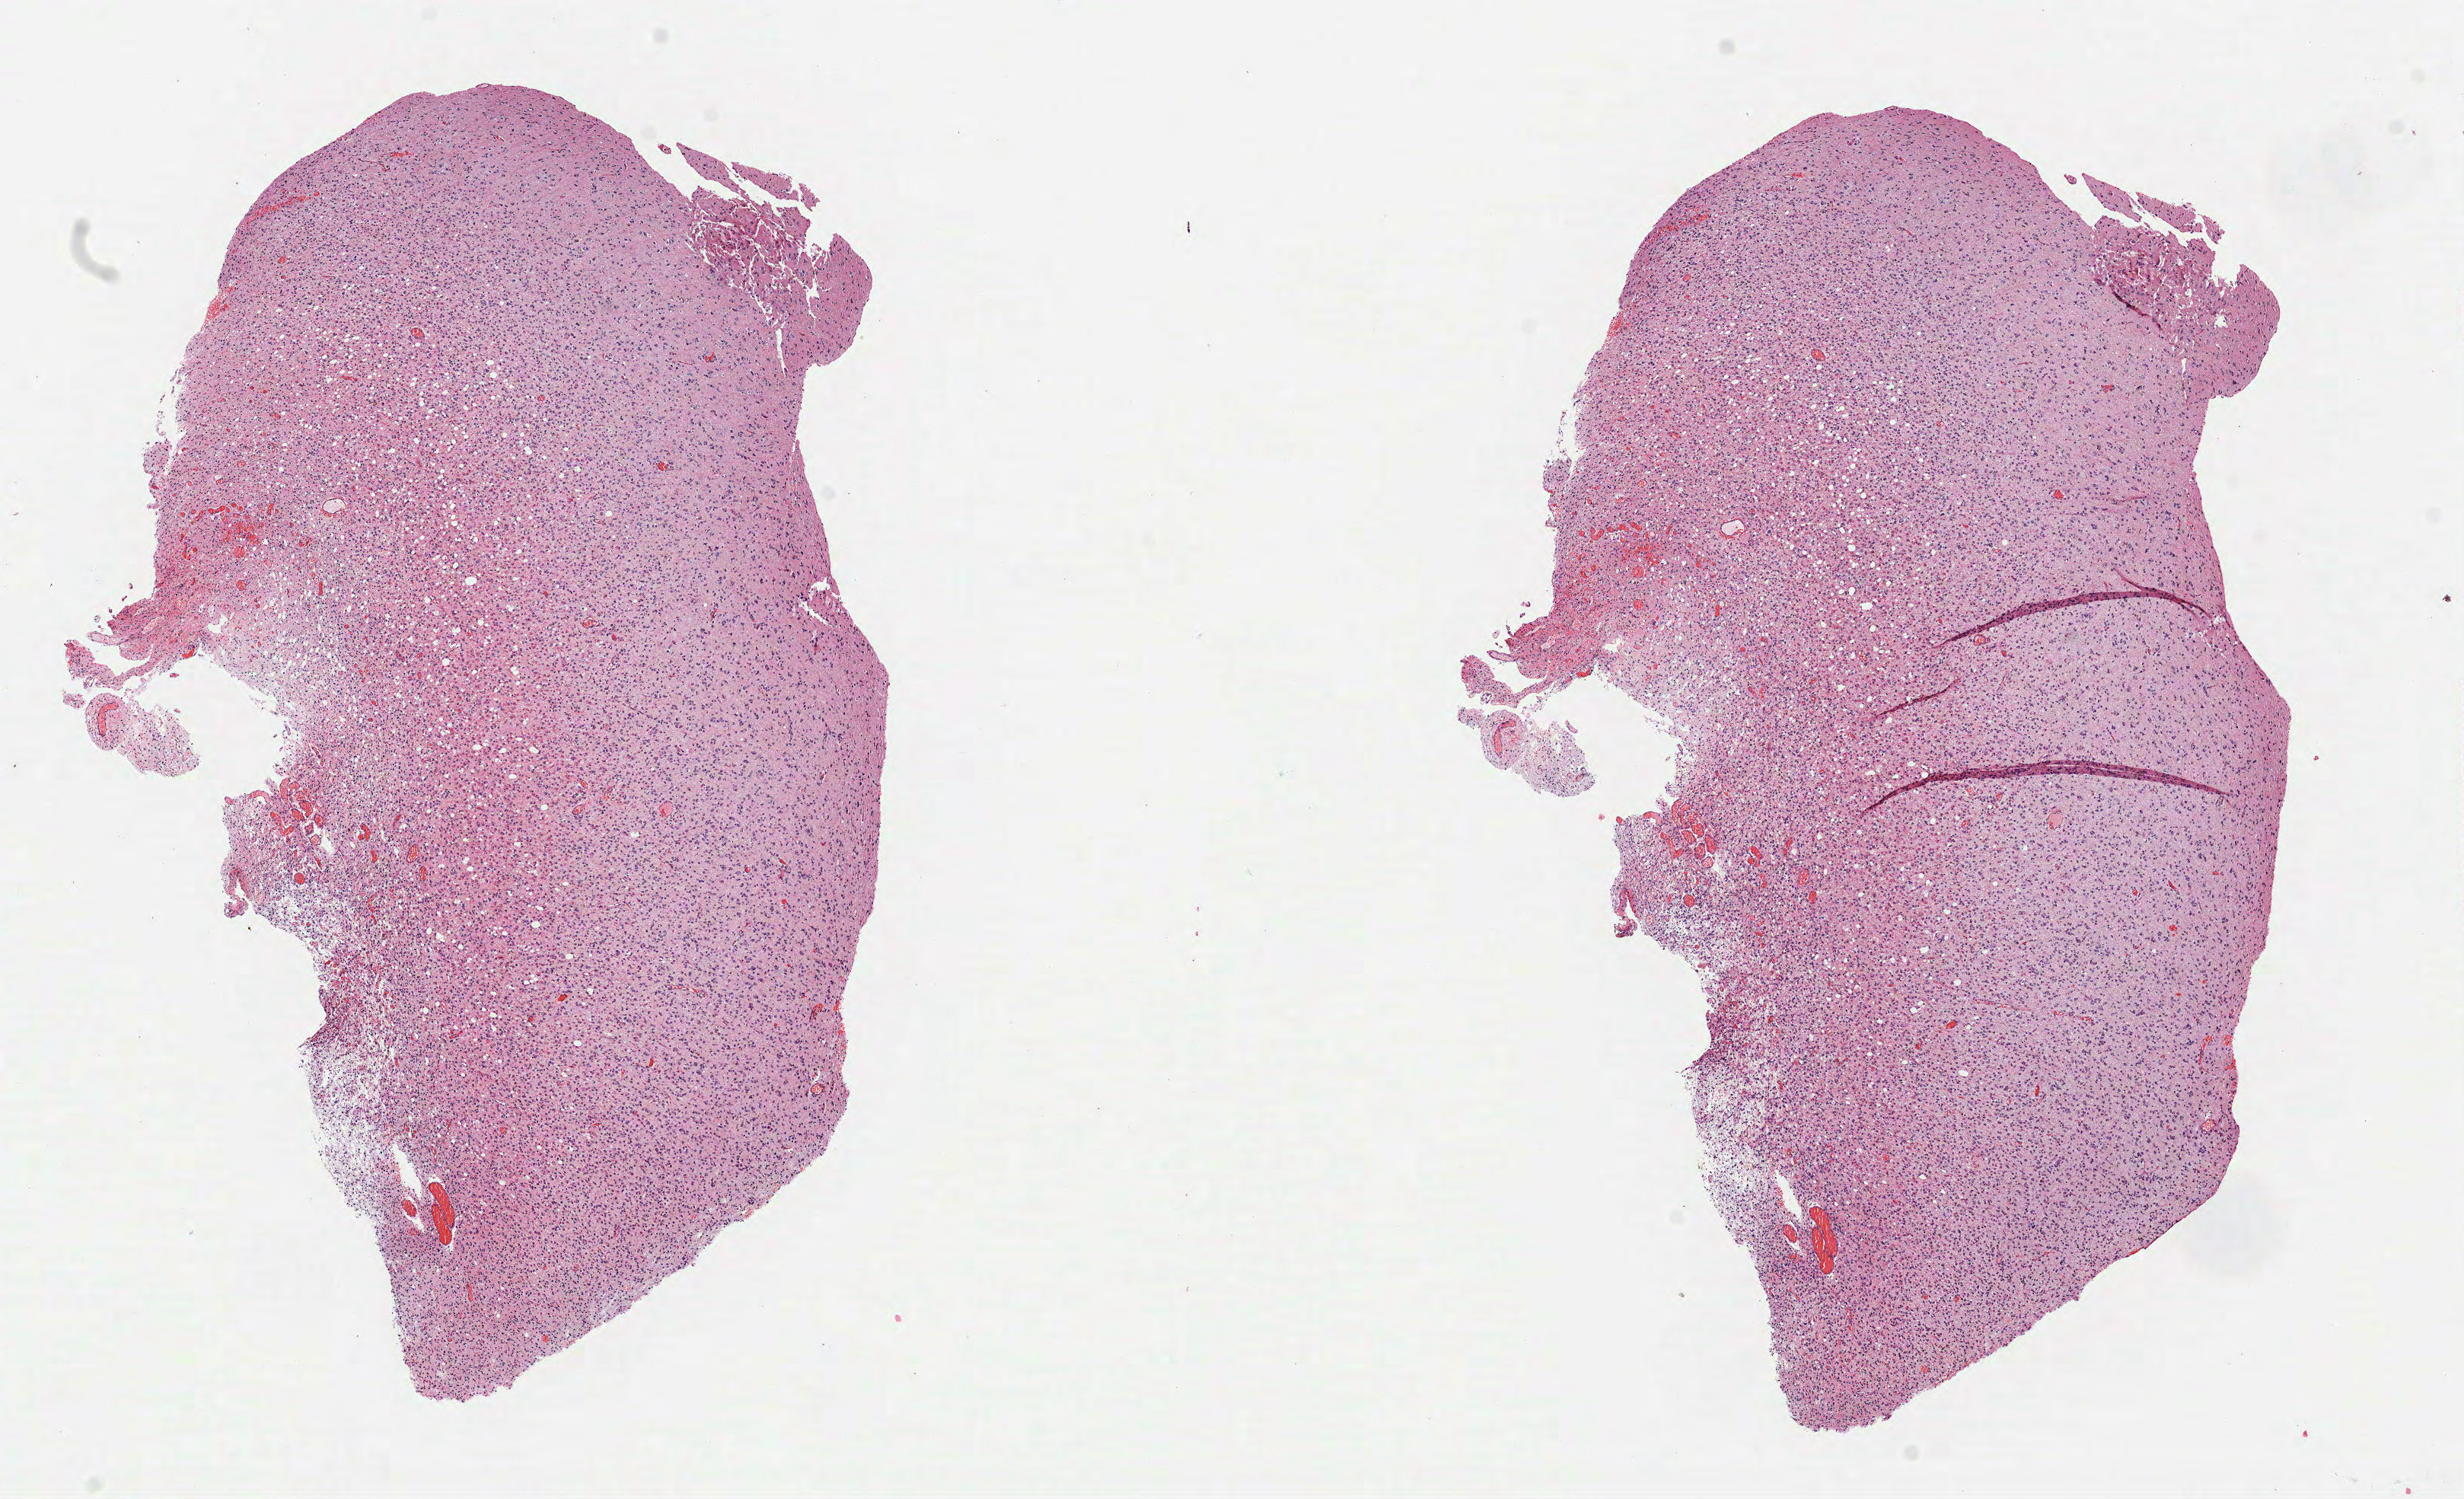
Hematoxylin and eosin (H&E) stained whole-slide image — a low-resolution overview of the entire scanned area, about 13.1 x 7.9 mm. Formalin-fixed paraffin-embedded (FFPE) diagnostic section. Primary tumour sample from the brain. Female patient; age at initial diagnosis 43 years. Histologic grade: G2 (moderately differentiated).
* pathologic diagnosis: Mixed glioma
* laterality: left